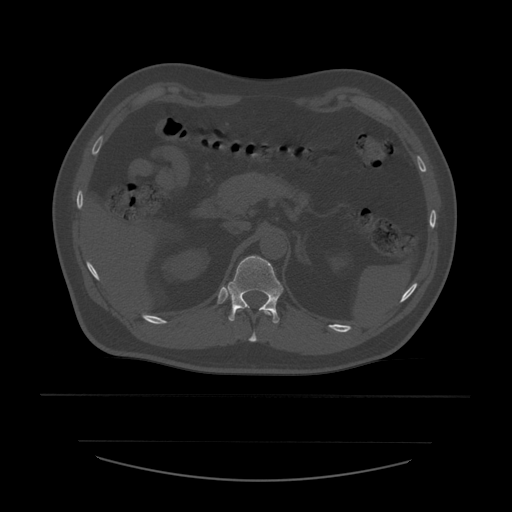
CT including the spine, one axial slice. Position 258 of 532 along the scan axis. Reconstruction kernel STANDARD. Bone window (W 1800 / L 400 HU). 1.25 mm slice thickness. 512 × 512 image matrix. Patient age 44 years. Case-level facts recorded for this patient, not image findings: primary cancer: soft tissue sarcoma.
Structures marked on this image (semi-automatically segmented with operator editing):
- T11 vertebra: bounding box (x1, y1, x2, y2) in pixels: (238, 310, 273, 342)
- T12 vertebra: (226, 256, 284, 324)